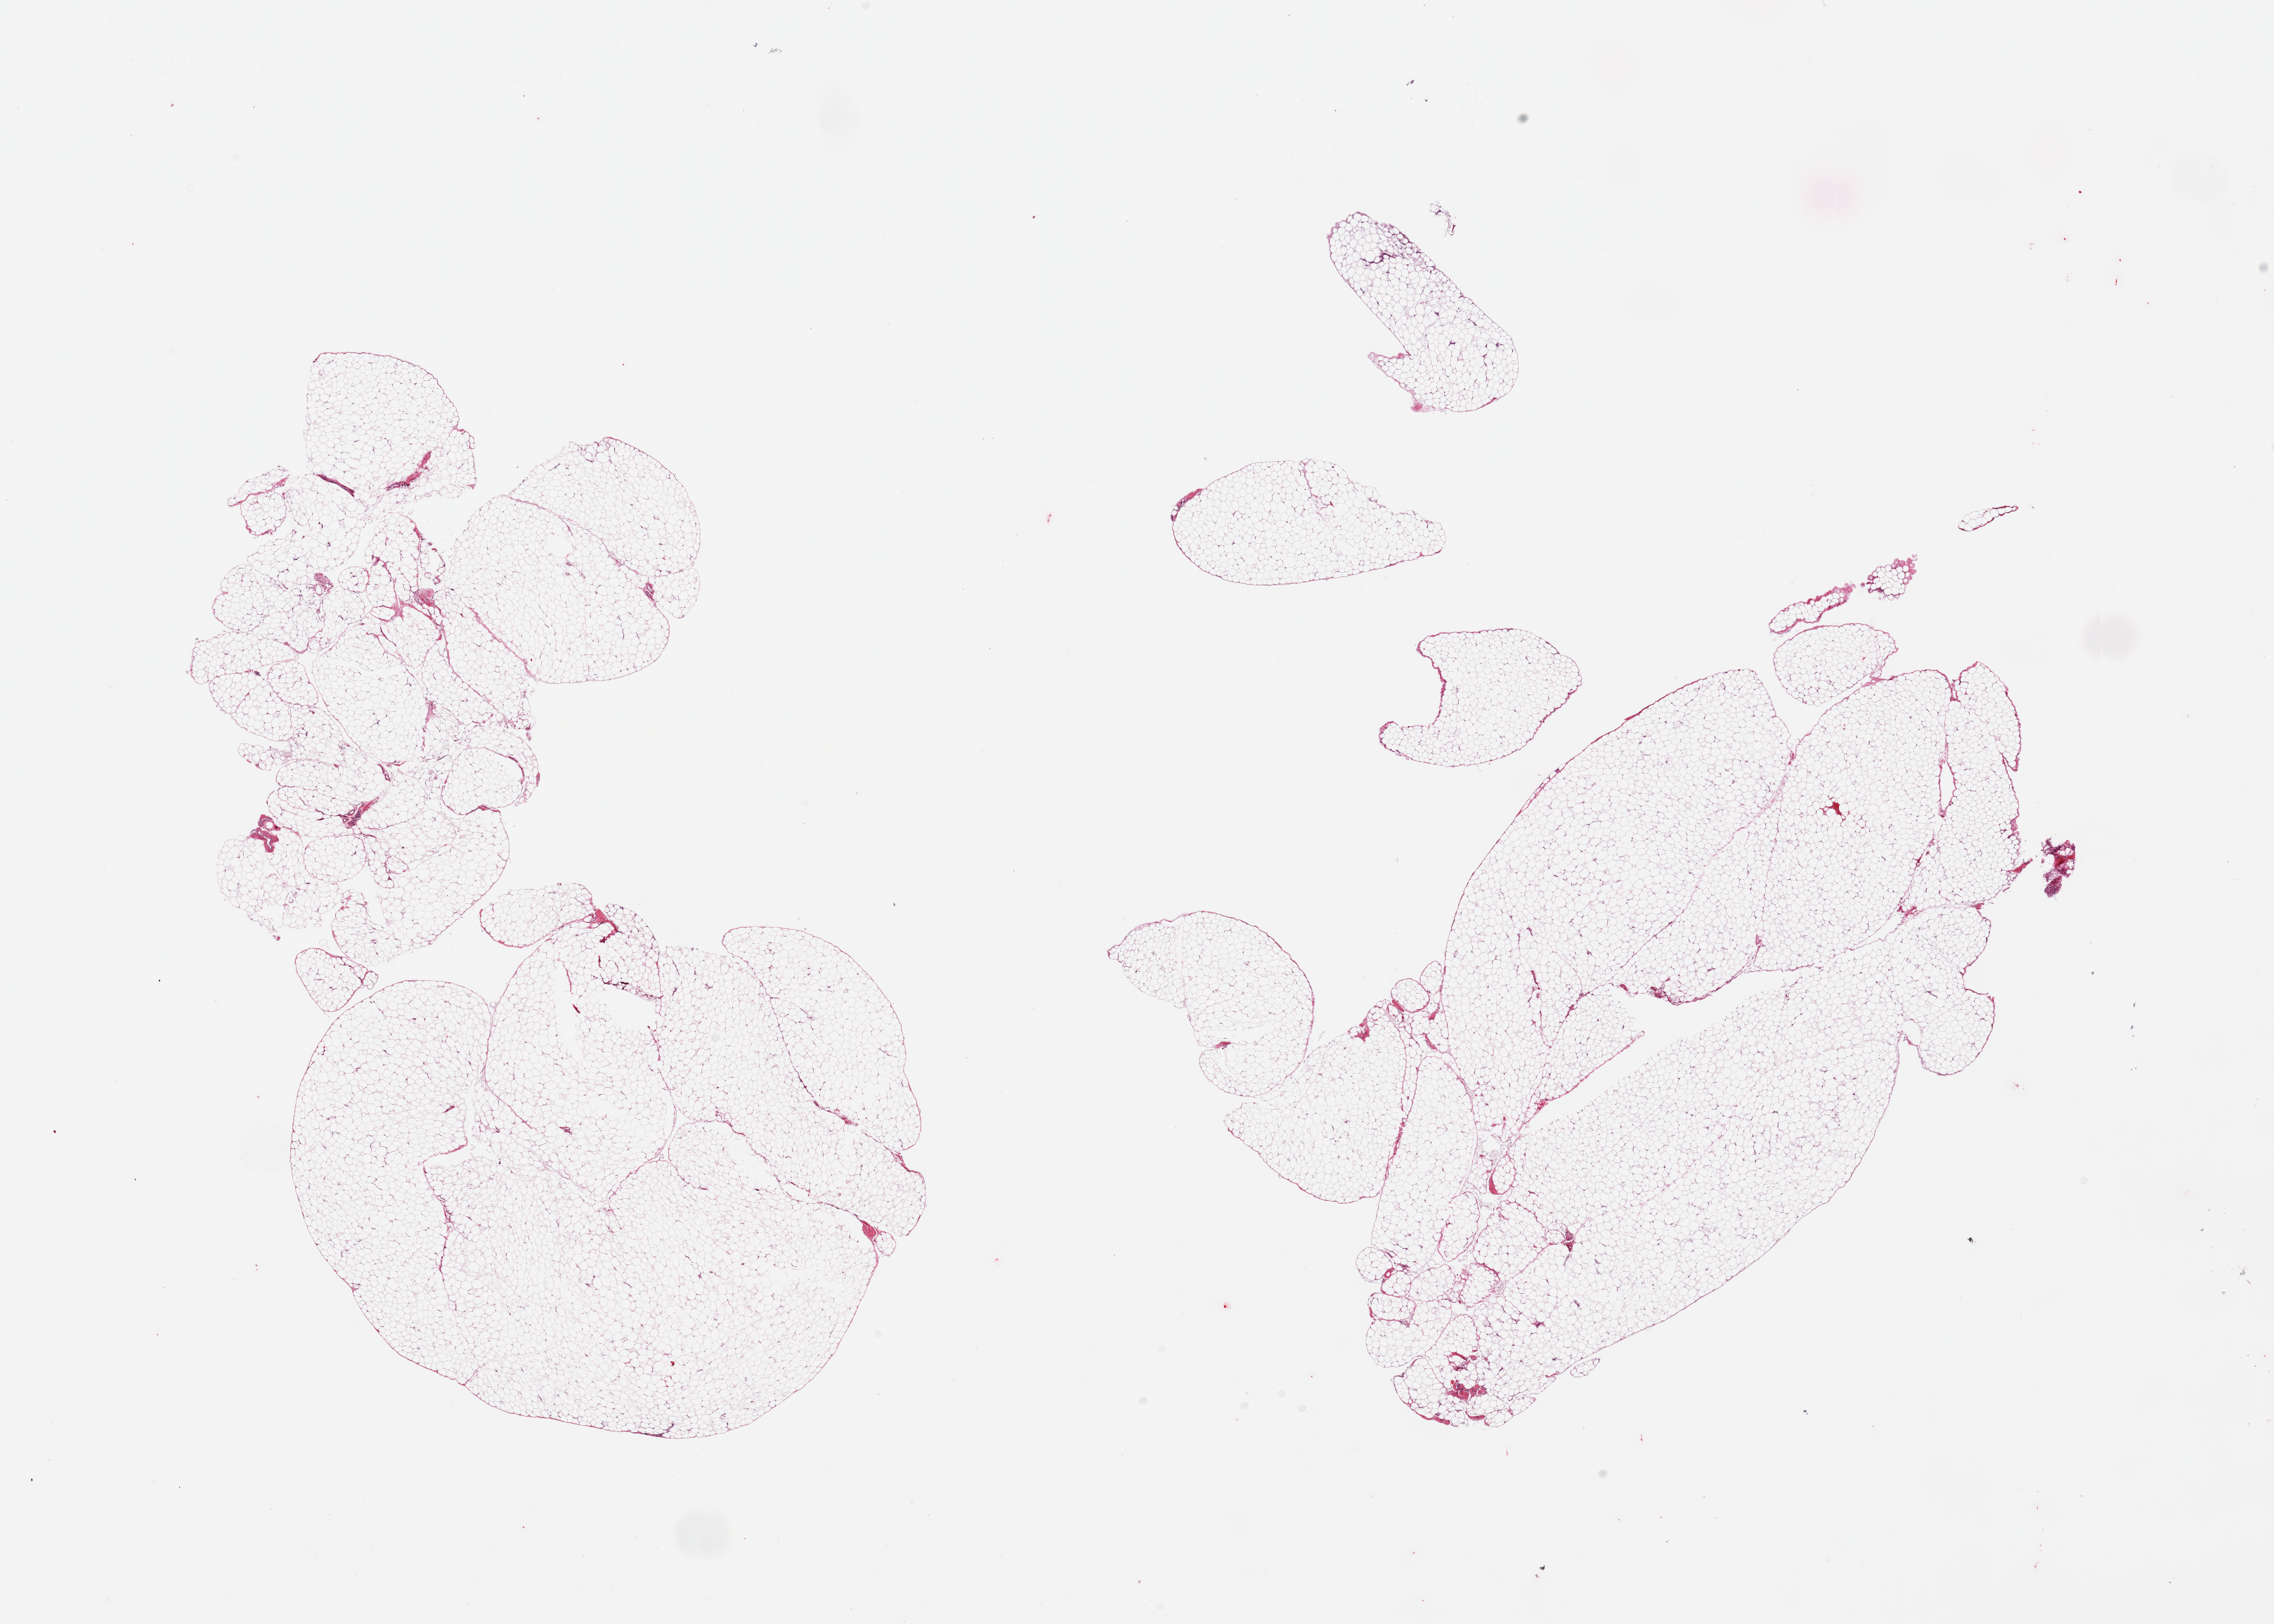
H&E whole-slide image, brightfield — low-resolution overview of the scanned area, about 25.6 x 18.3 mm, PAXgene-fixed paraffin-embedded (PFPE) section, section of omentum (target tissue), tissue donor sample.
Pathologist's review note for this sample: 2 pieces; minimal fibrous content.